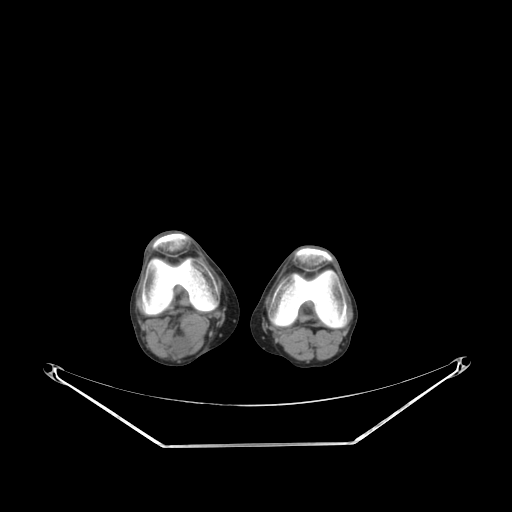
CT of an extremity soft-tissue mass (from a PET/CT study), one axial slice; slice 162 of 267 in the series (ordered by position); reconstruction kernel SOFT; 140 kVp; soft-tissue window (W 400 / L 40 HU); 3.75 mm slice thickness; 512 × 512 image matrix. Female patient. Case-level facts recorded for this patient, not image findings: histological type: liposarcoma; site of the primary tumour: right thigh.
Structures marked on this image (expert contour drawn on MRI and transferred to this co-registered scan by the dataset authors):
- gross tumour volume (mass): box from (x=169, y=336) to (x=190, y=355) px